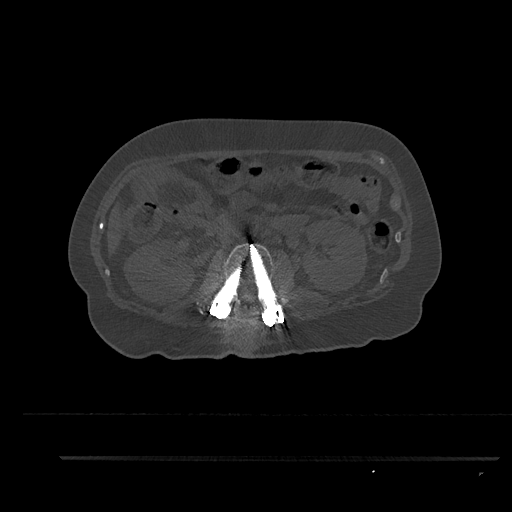
CT including the spine, one axial slice; slice 167 of 797 in the series (ordered by position); reconstruction kernel Br40s/3; 120 kVp; bone window (W 1800 / L 400 HU); 512 × 512 image matrix. Female patient, age 44 years. From the clinical record (not read from this slice): primary cancer: renal; vertebrae with lytic lesions (as recorded): L1.
Outlined on this slice (semi-automatic segmentation, software-assisted and operator-edited):
- L2 vertebra: bounding box (x1, y1, x2, y2) in pixels: (206, 243, 284, 320)